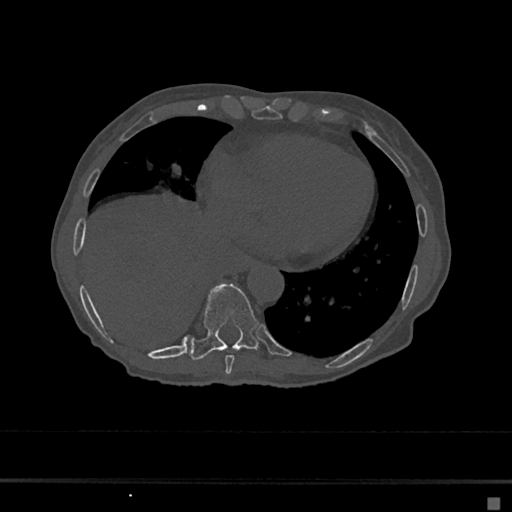
CT including the spine, one axial slice; position 283 of 797 along the scan axis; reconstruction kernel Br40s/3; bone window (W 1800 / L 400 HU); 0.5 mm slice thickness; 512 × 512 image matrix, field of view 360 × 360 mm. Patient: female, 68 years. Case-level facts recorded for this patient, not image findings: primary cancer: renal.
Annotated regions visible in this slice (semi-automatically segmented with operator editing):
- T8 vertebra: bounding box <225,355,235,375> (left, top, right, bottom; pixels)
- T9 vertebra: <190,283,259,360>